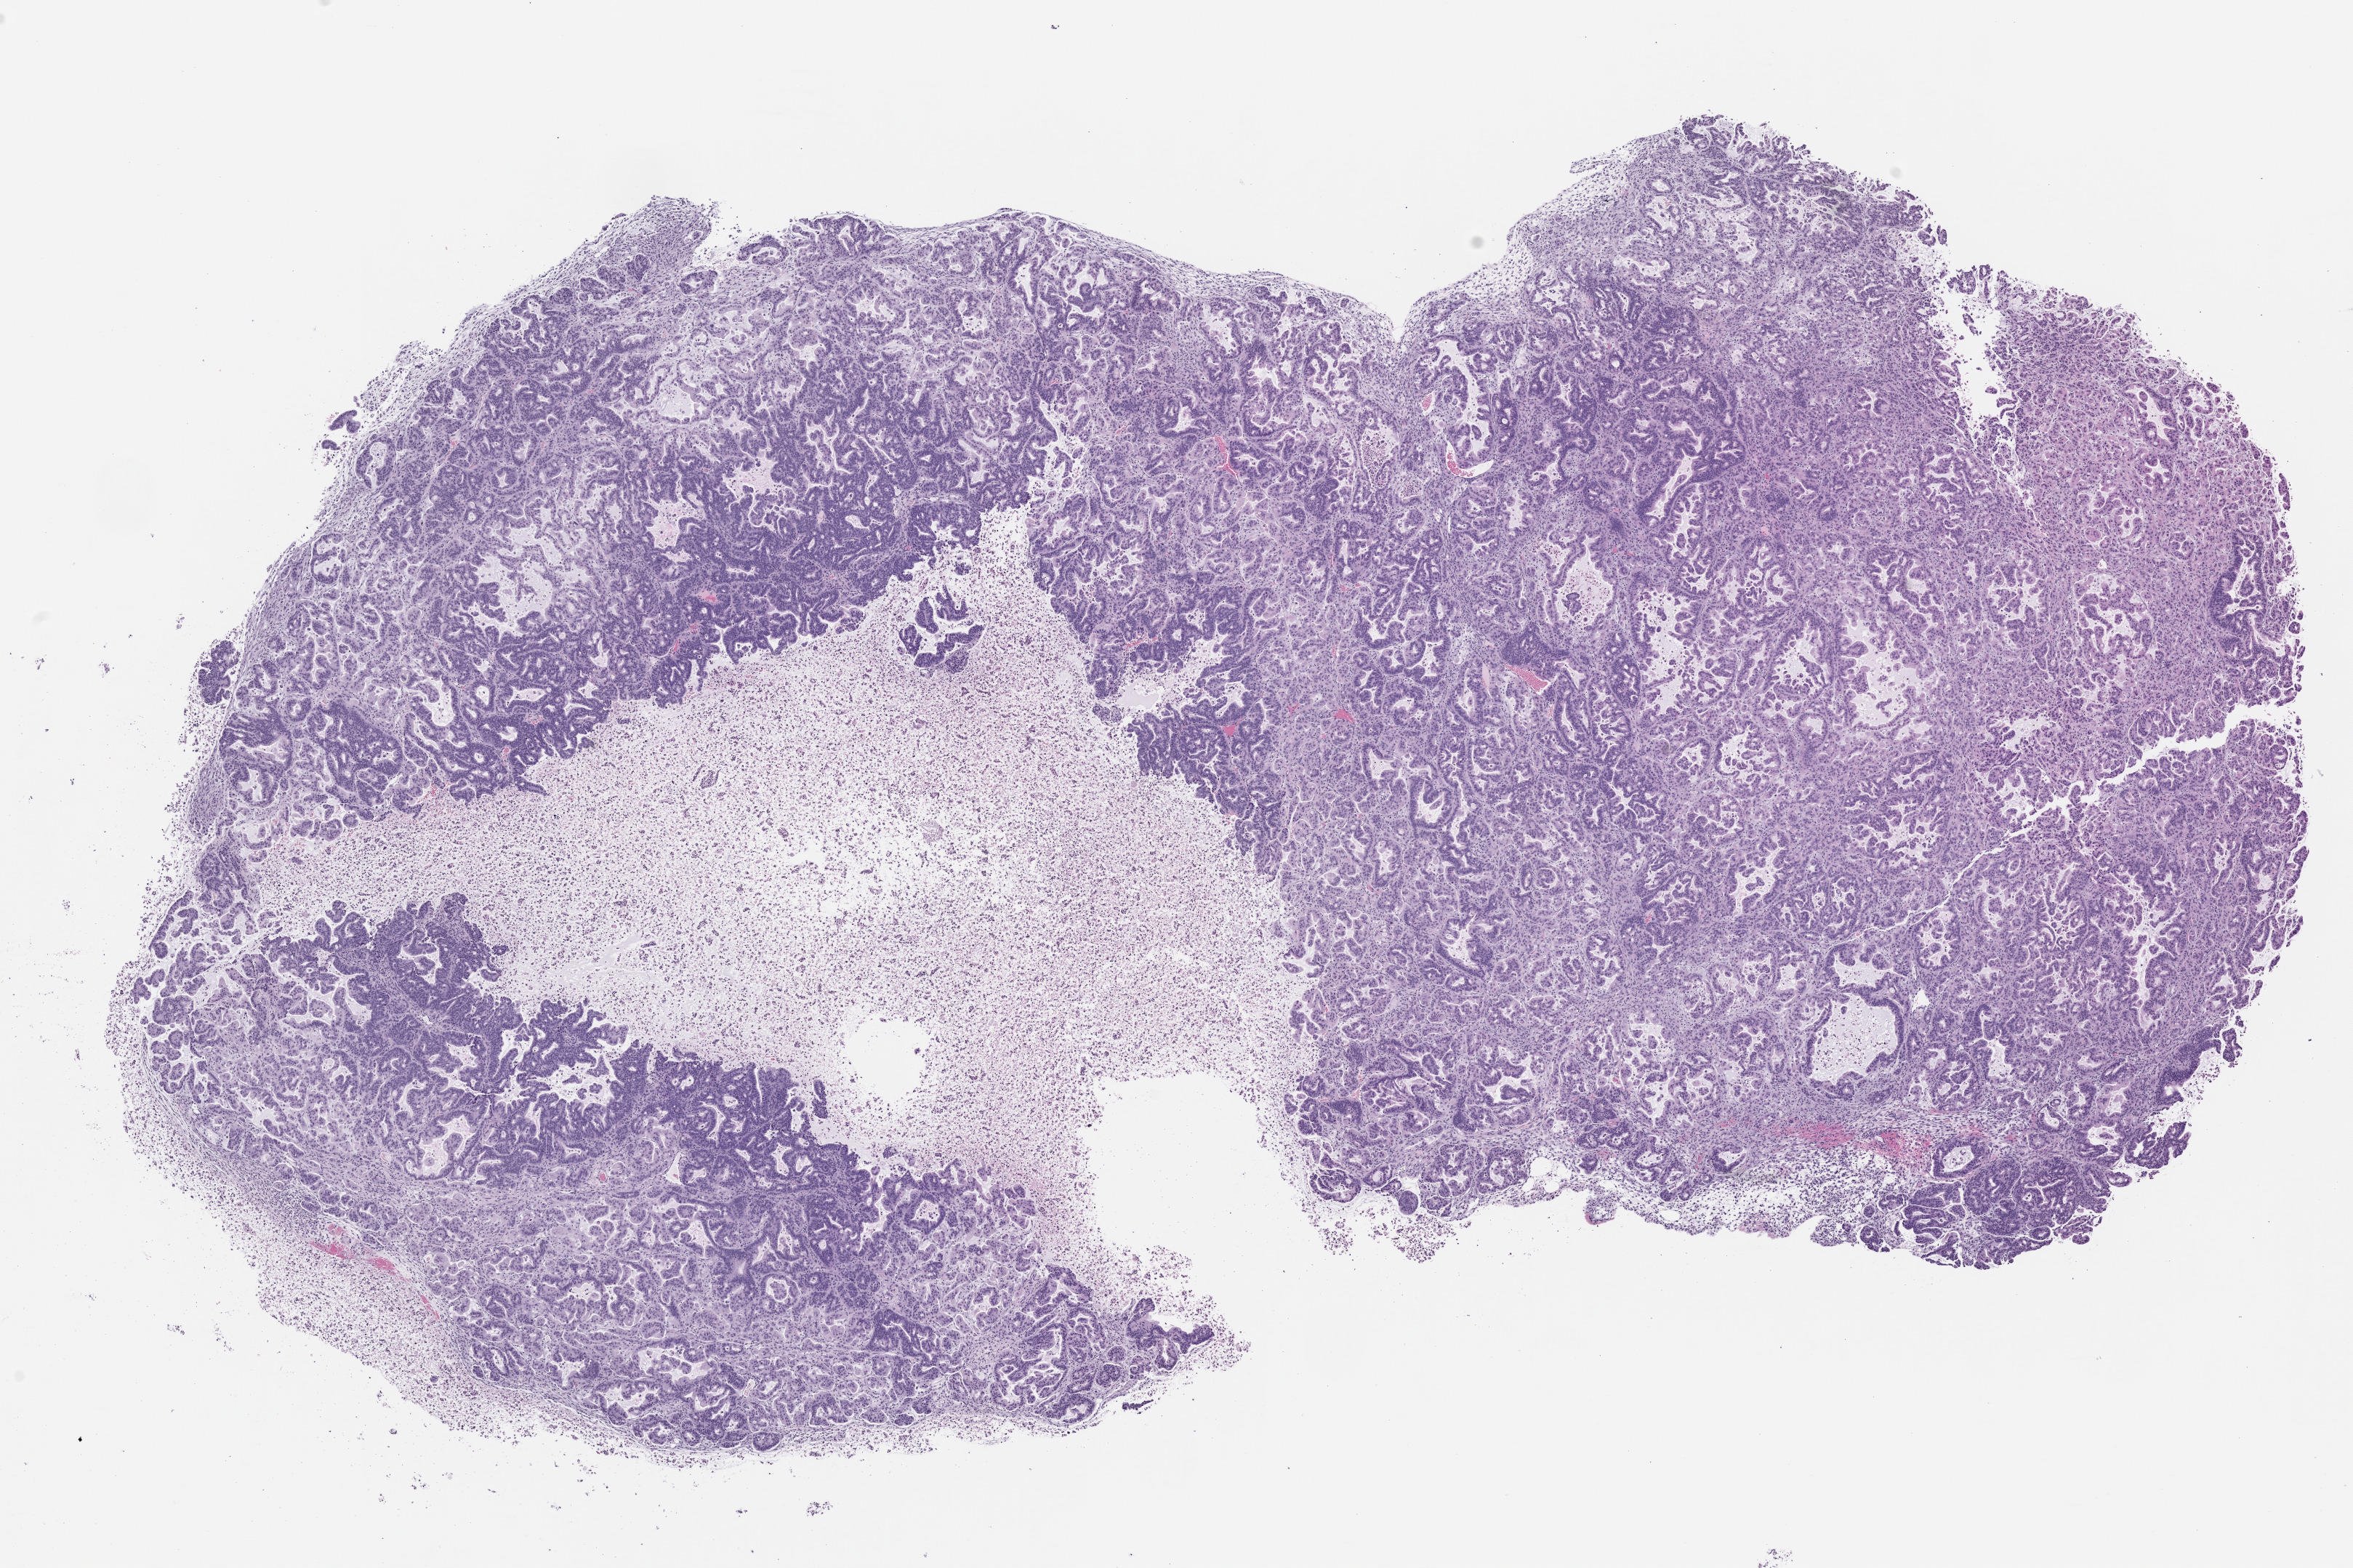
Whole-slide image, H&E: patient-derived xenograft (human tumor grown in a mouse), passage 1, low-resolution overview of the scanned area, about 13.0 x 8.7 mm. Formalin-fixed paraffin-embedded section. Originating tumor site category: pancreas.
Originating patient diagnosis: Pancreatic Adenocarcinoma.